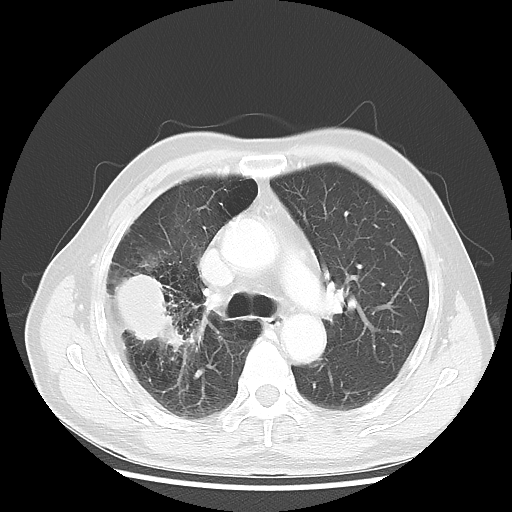
Chest CT, one axial slice; slice 32 of 50 in the series (ordered by position); reconstruction kernel LUNG; 120 kVp; lung window (W 1500 / L -600 HU); 5 mm slice thickness; 512 × 512 image matrix, field of view 360 × 360 mm. Patient: male, 69 years. Case-level facts recorded for this patient, not image findings: clinical TNM (as recorded): T3 N0 M0; histopathological grade: G3.
Outlined on this slice (bounding box drawn by a radiologist):
- lung tumour (recorded histology: adenocarcinoma): bounding box <111,273,185,352> (left, top, right, bottom; pixels)